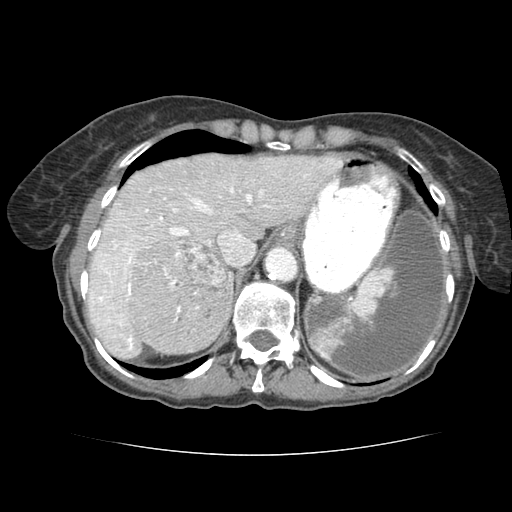
Contrast-enhanced abdominal CT (liver protocol), one axial slice. Position 61 of 77 along the scan axis. Reconstruction kernel STANDARD. 120 kVp. Soft-tissue window (W 400 / L 40 HU). 2.5 mm slice thickness. 512 × 512 image matrix, field of view 340 × 340 mm. From the clinical record (not read from this slice): diagnosis: hepatocellular carcinoma (patient treated with transarterial chemoembolisation; whether this scan precedes or follows treatment is not stated here); TNM stage (as recorded): Stage-I; Child-Pugh class: A; tumour differentiation: well differentiated.
Annotated regions visible in this slice (semi-automatically segmented with operator editing):
- liver parenchyma outside the tumour (the mass and vessels are separate outlines, so this box may not span the whole liver): bounding box (x1, y1, x2, y2) in pixels: (82, 152, 336, 353)
- mass: (125, 237, 230, 348)
- liver vessels: (91, 194, 230, 319)